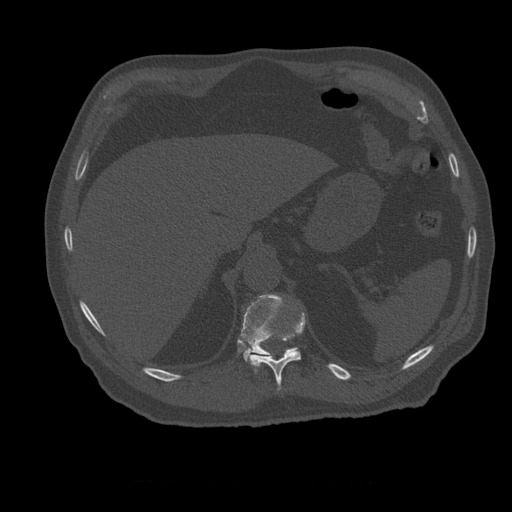
CT including the spine, one axial slice. 120 kVp. Bone window (W 1800 / L 400 HU). 1.25 mm slice thickness. 512 × 512 image matrix. Patient age 73 years. Case-level facts recorded for this patient, not image findings: primary cancer: prostate.
Structures marked on this image (semi-automatic segmentation, software-assisted and operator-edited):
- T11 vertebra: bounding box [x1, y1, x2, y2] px = [250, 313, 306, 391]
- T12 vertebra: [239, 295, 299, 363]